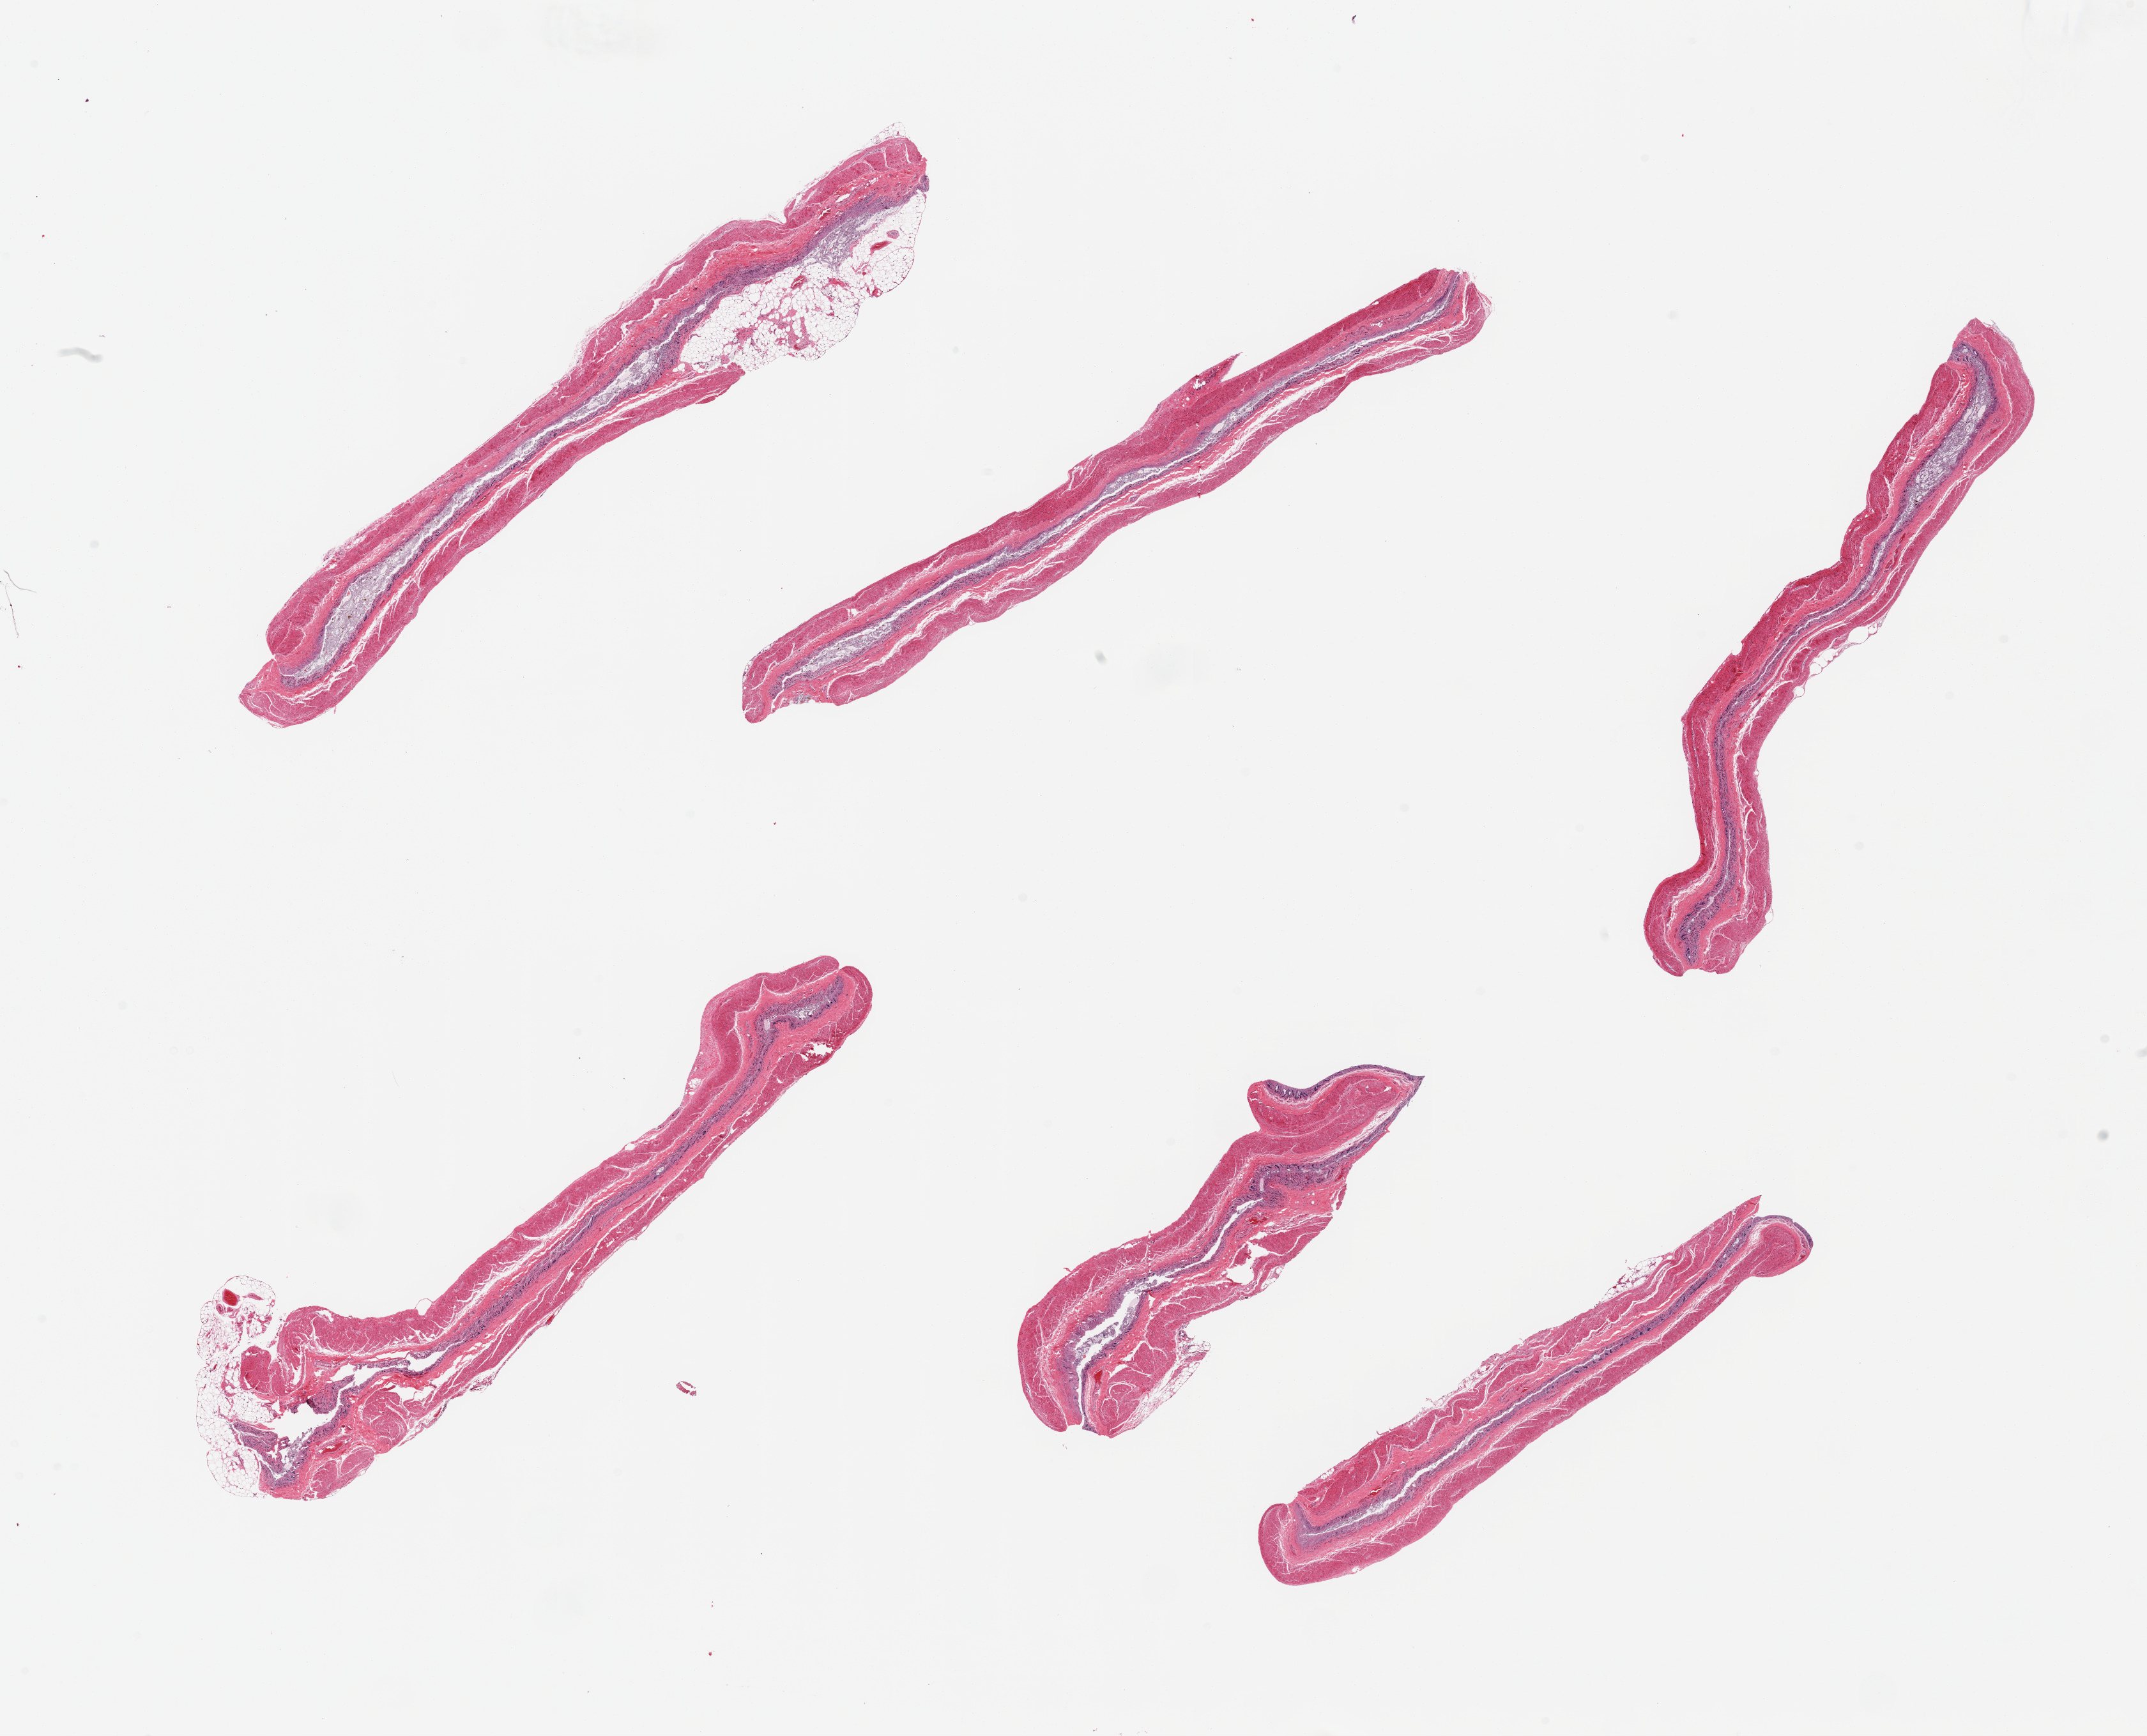
Digitized hematoxylin and eosin (H&E)-stained section, shown as a low-resolution overview of the whole scanned area (about 26.6 x 21.5 mm); PAXgene-fixed, paraffin-embedded tissue; sampled site (target tissue): transverse colon; tissue donor sample. Donor: male.
Pathologist's review note for this sample: 6 pieces, mucosa totally autolyzed.